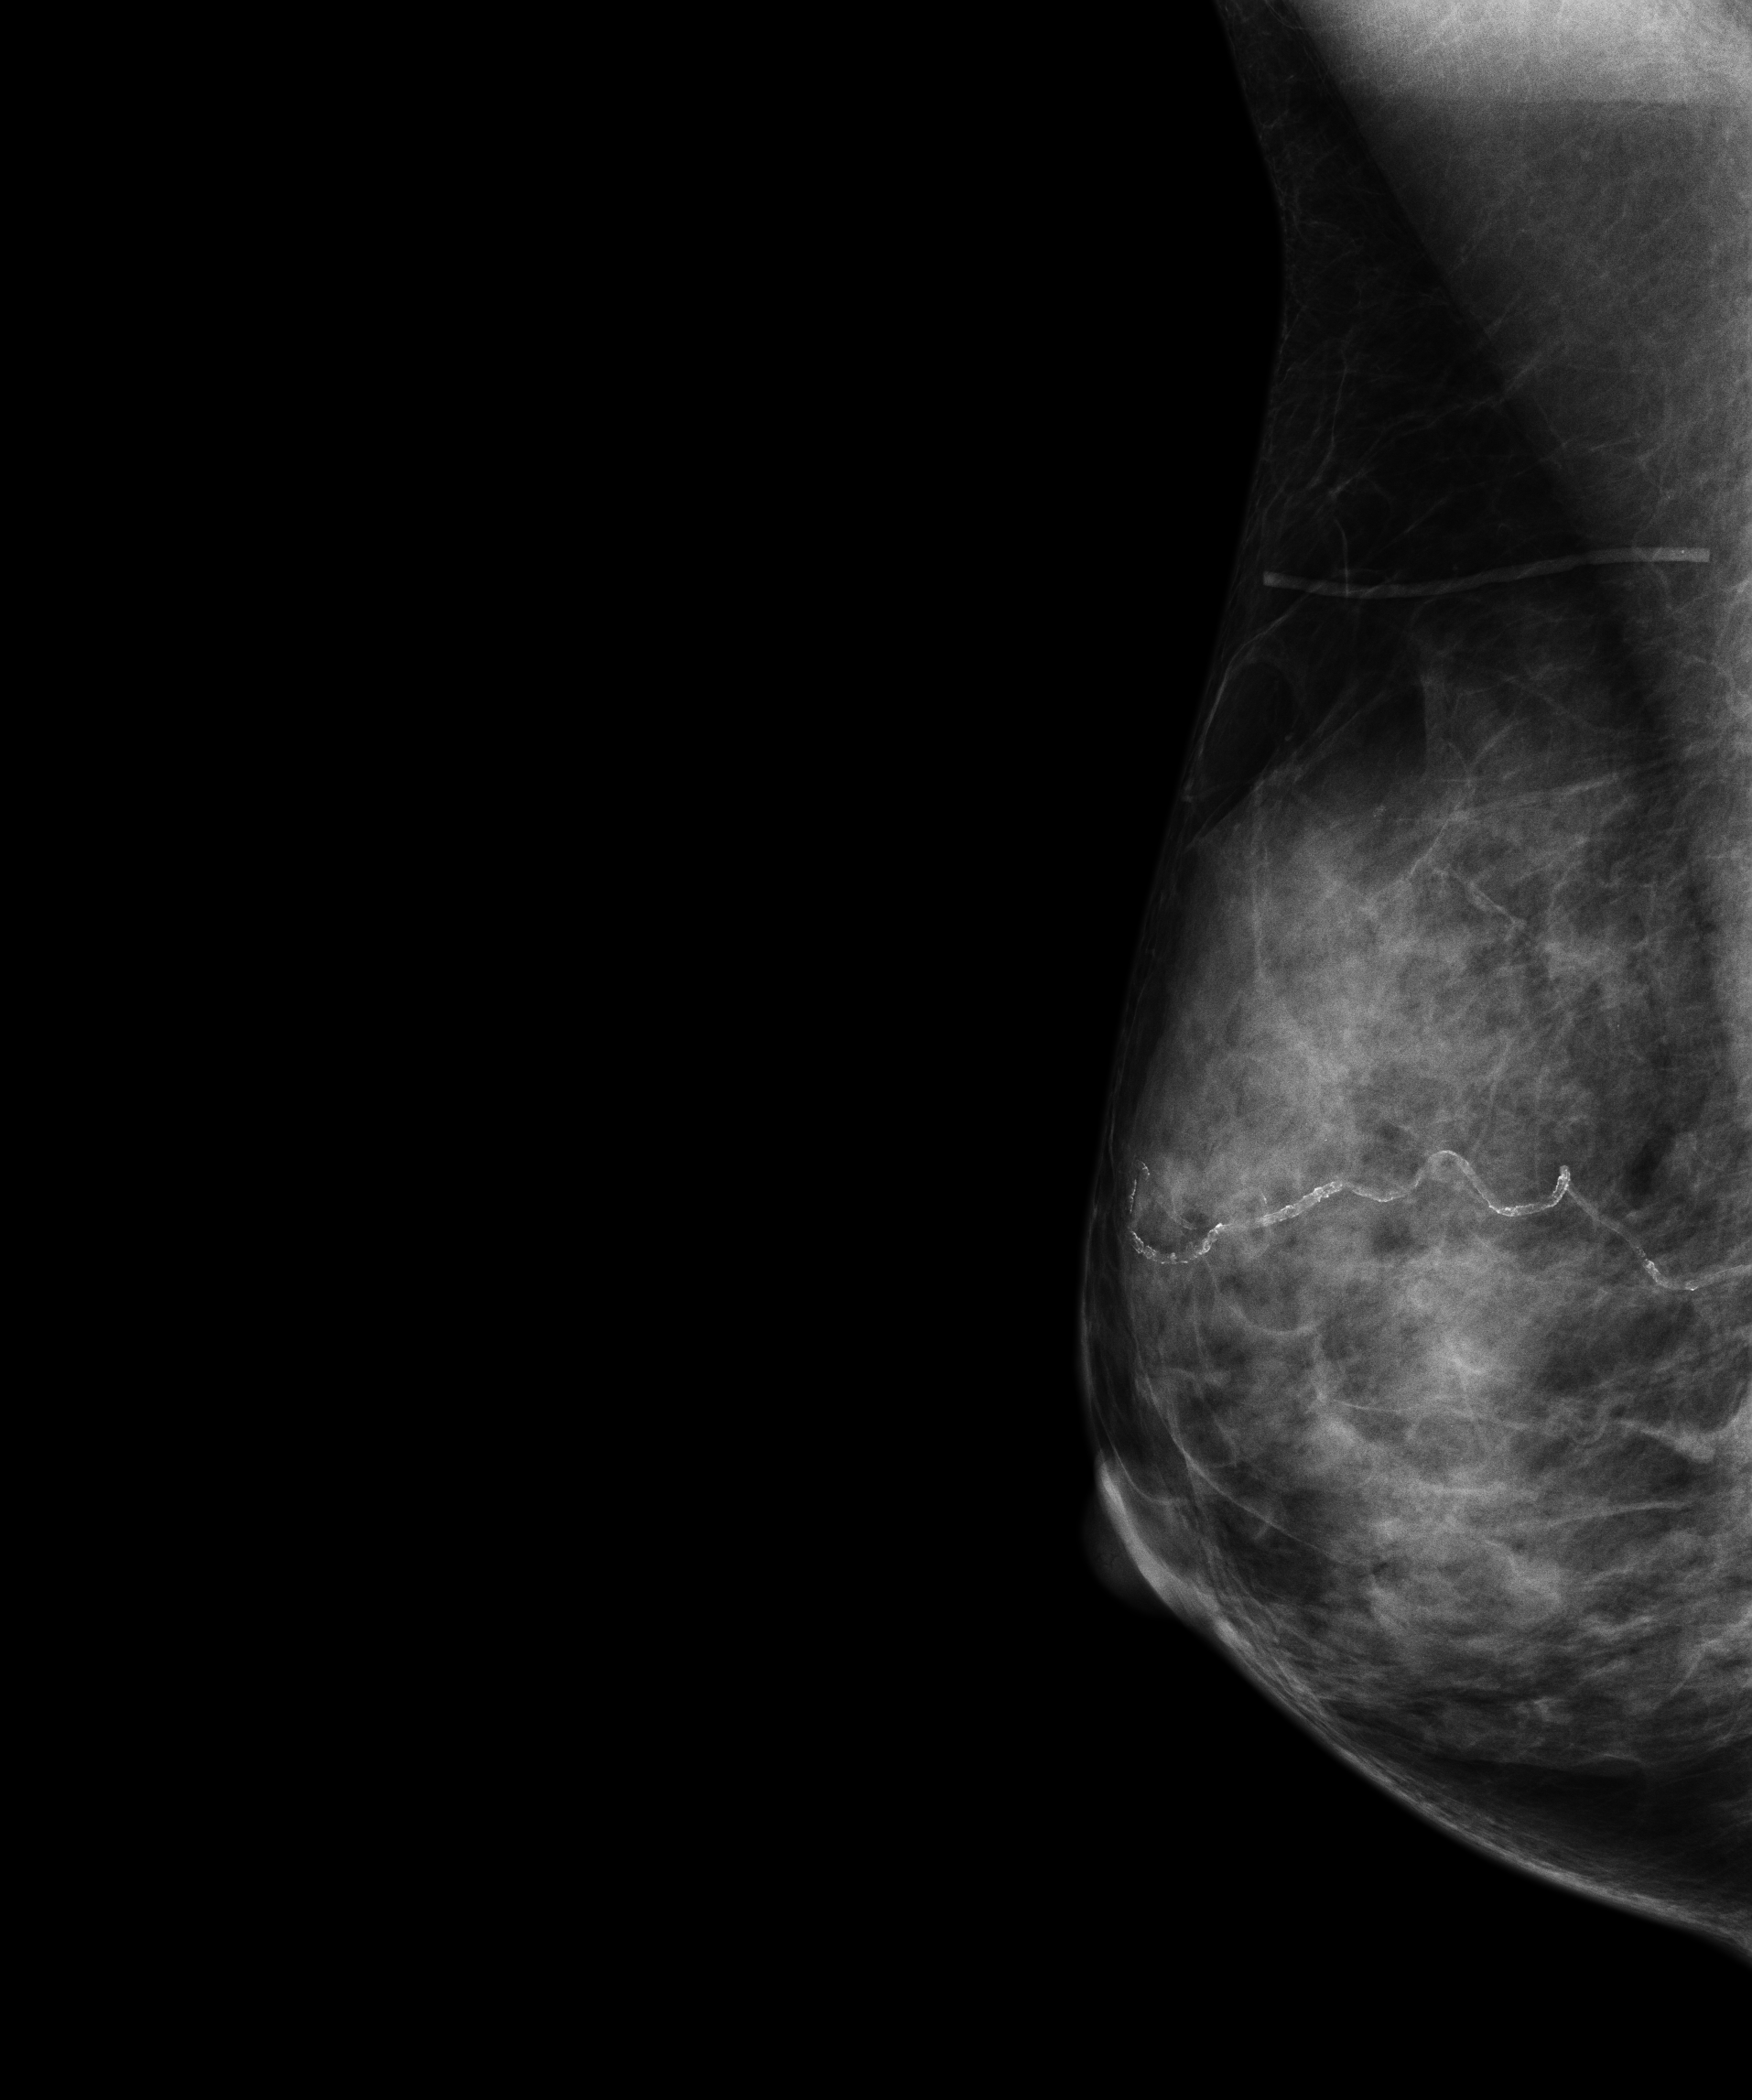
Annual screening mammography examination, system: Senographe Essential ADS_56.21.3. Female patient, age 60 years.
Image type: full-field digital mammogram. Breast: right. Projection: medio-lateral oblique projection.